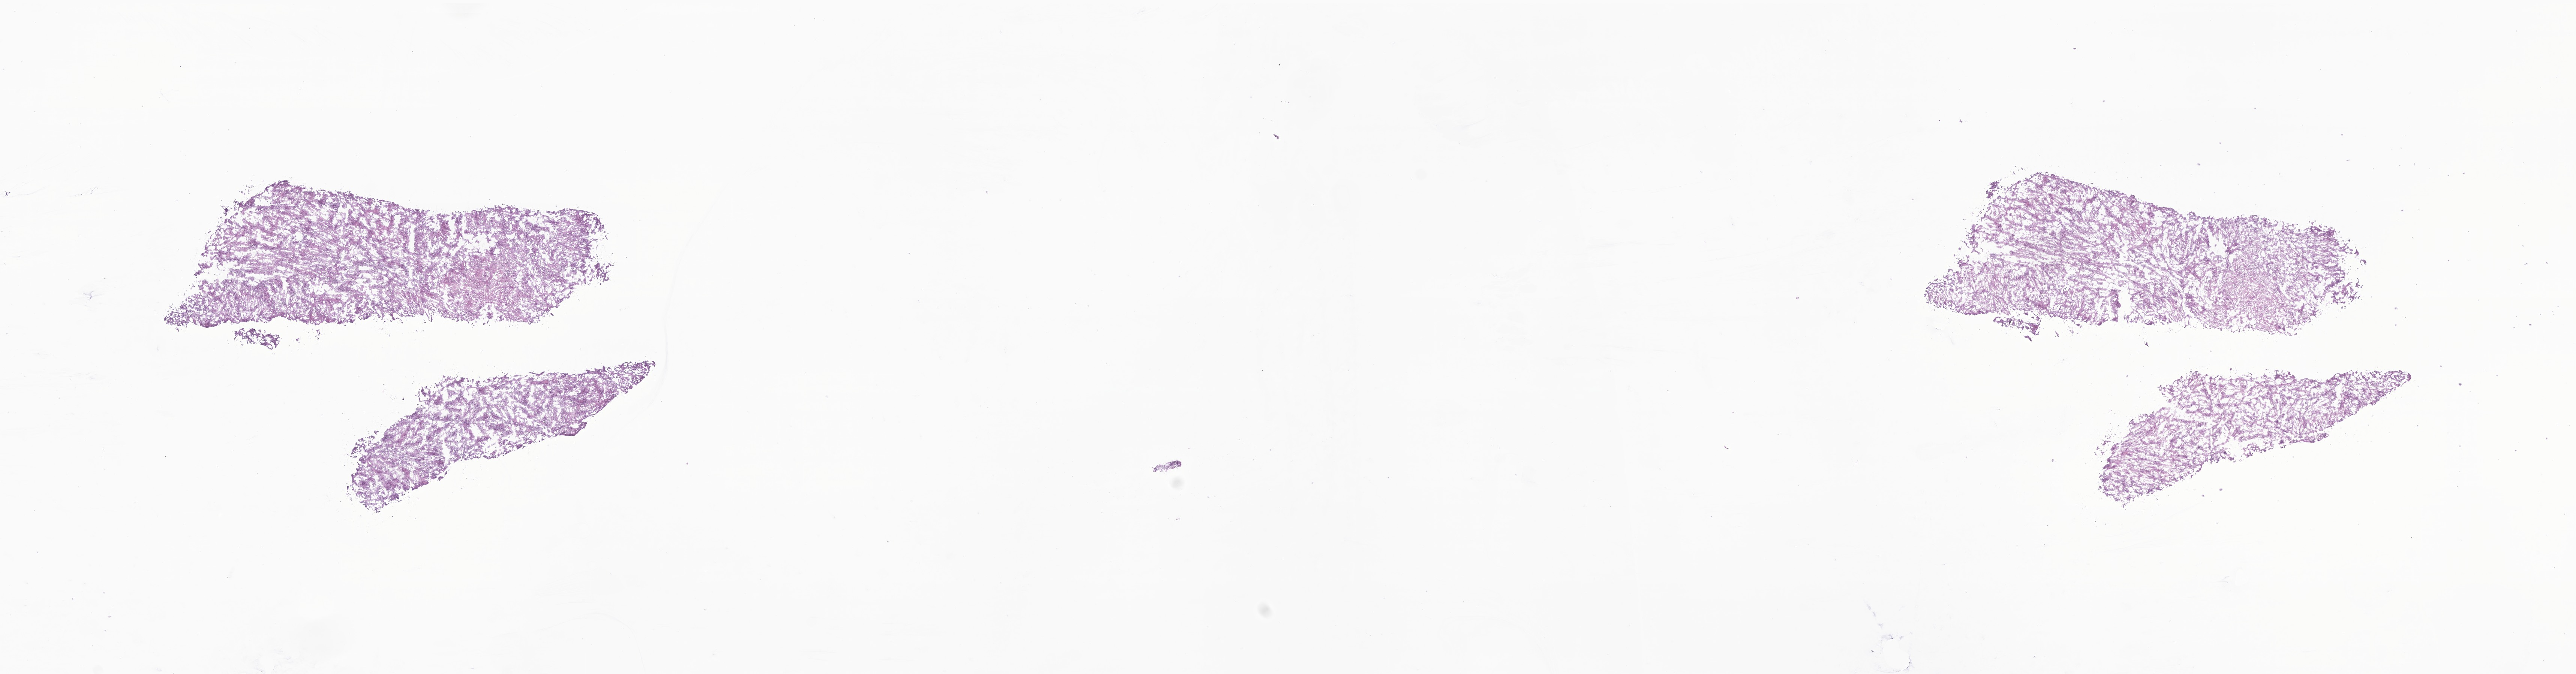
Whole-slide image, haematoxylin and eosin stain of tumor tissue from the frontal lobe, low-resolution overview of the scanned area, about 29.0 x 7.6 mm. Frozen section. Female patient, age 176 months (14 years 8 months).
Diagnosis (ICD-O-3 morphology term): Ganglioglioma, NOS.